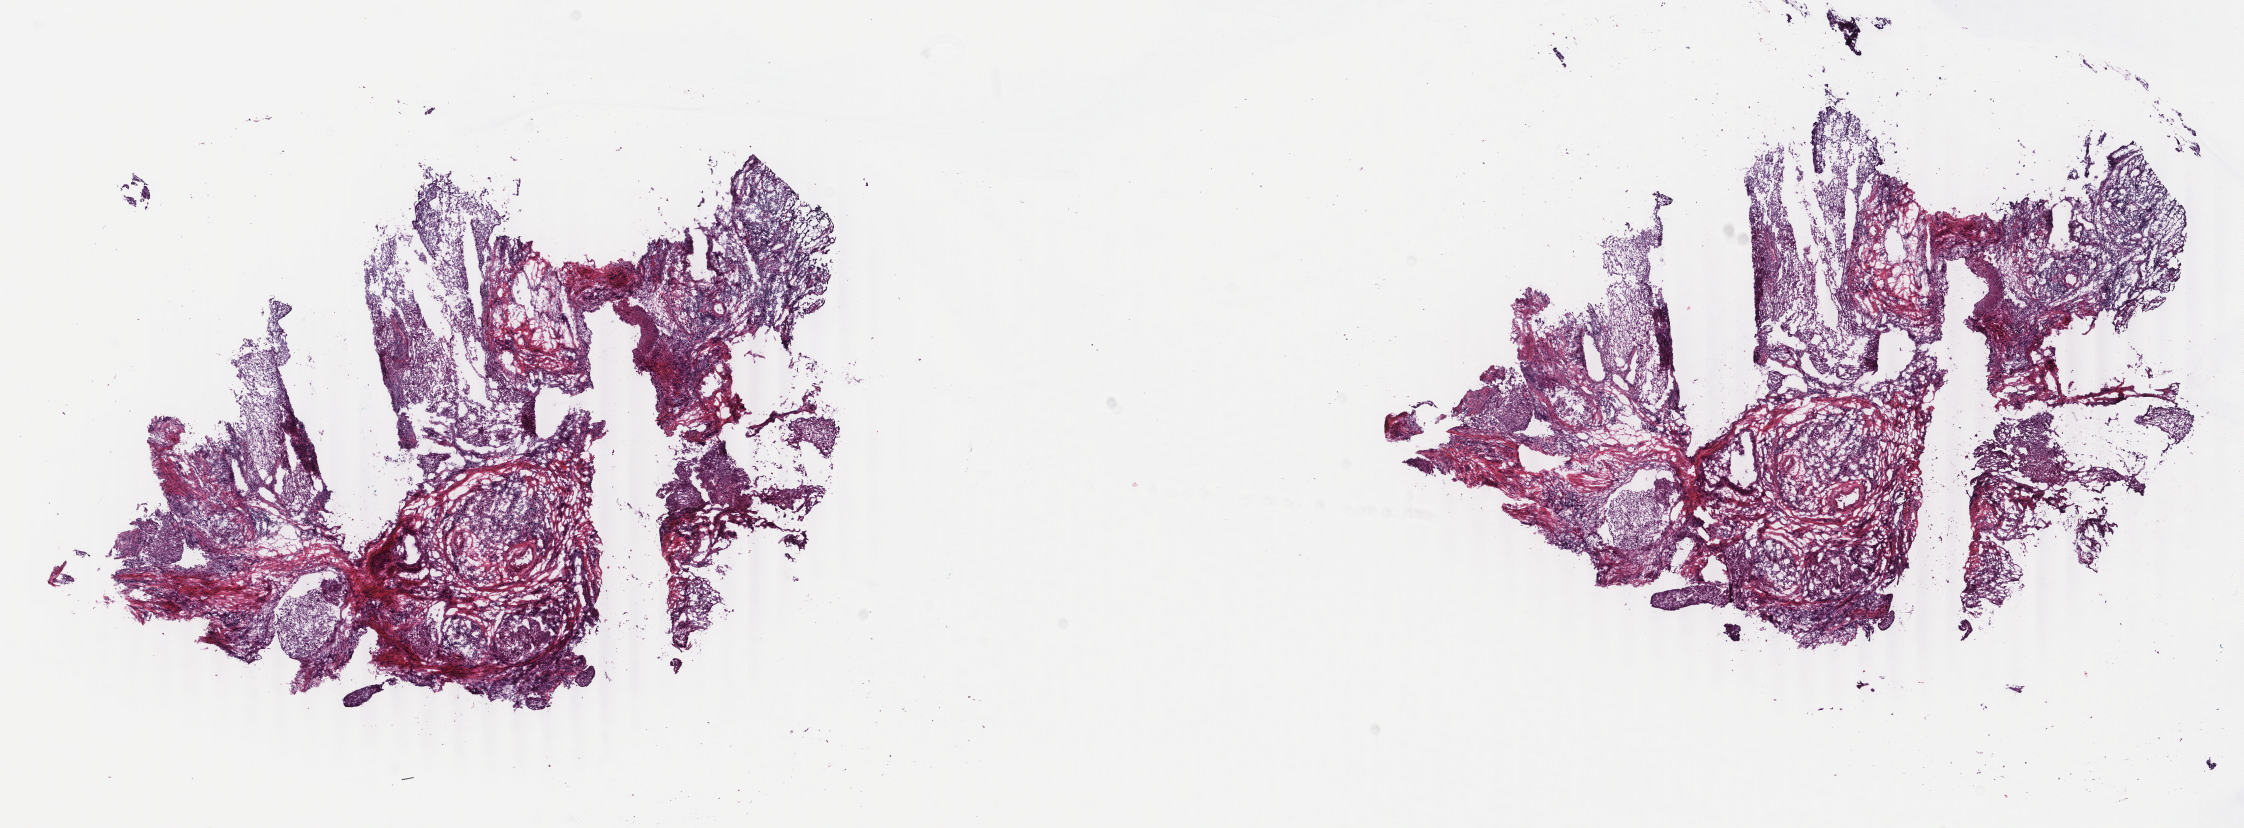
Digitized Hematoxylin and eosin (H&E) stained tissue section (whole slide) — whole scanned area (about 17.8 x 6.6 mm) shown as a low-resolution overview, frozen section from the bottom of the tissue portion, cervix, primary tumour sample. Female, age 61 years at initial diagnosis. Histologic grade: G2 (moderately differentiated). Pathologist review of this section (percent, as recorded): tumour cells 60%, tumour nuclei 60%, normal cells 0%, stromal cells 40%, necrosis 0%. Inflammatory infiltration, as recorded: lymphocyte infiltration 25%, monocyte infiltration 0%, neutrophil infiltration 2%.
FIGO stage: IIIB. Diagnosis: Squamous cell carcinoma, NOS (cervix uteri).